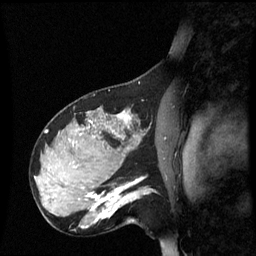
Breast MRI (dynamic contrast-enhanced), one sagittal slice. Slice 39 of 60 in the series (ordered by position). Dynamic contrast-enhanced series, image 2 of 3 at this slice position (ordered by acquisition). 1.5 T. TE 4.2 ms, TR 8.9 ms. 2.2 mm slice thickness. 256 × 256 image matrix, field of view 220 × 220 mm. Female patient, age 31 years. From the clinical record (not read from this slice): setting: breast cancer imaged before/during neoadjuvant chemotherapy; receptor status: HR-positive, HER2-negative.
Structures marked on this image (semi-automatic segmentation, software-assisted and operator-edited):
- analysis volume of interest (the breast-tissue region the enhancement analysis was run in; not a lesion): bounding box [x1, y1, x2, y2] px = [90, 180, 152, 227]
- tumour enhancement mask (voxels above the 70 % enhancement threshold inside the analysis volume of interest): [90, 180, 147, 223]